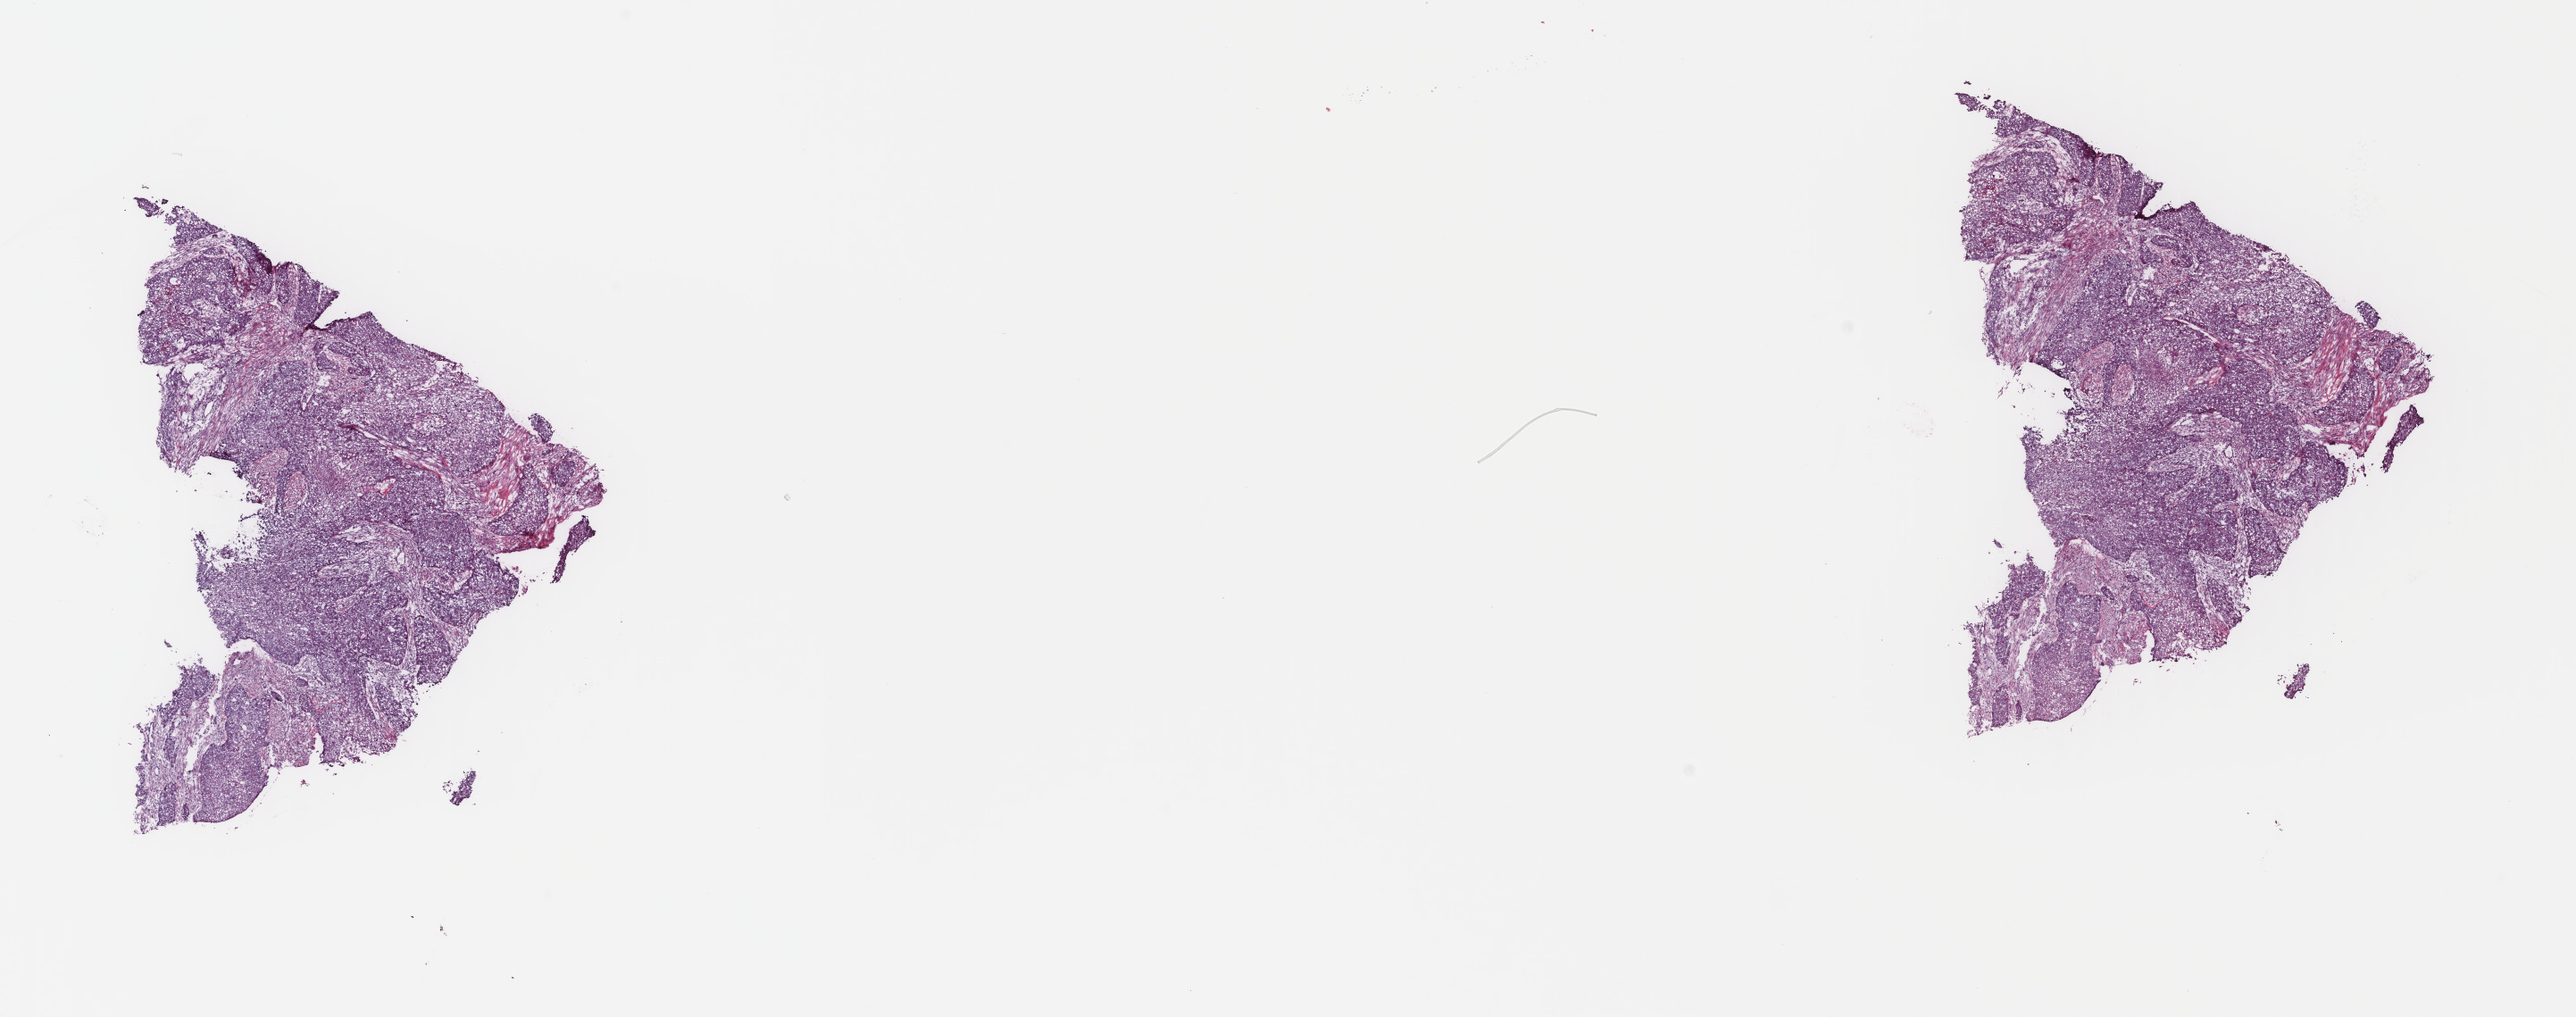
Whole-slide histology image, H&E-stained, a low-resolution overview of the entire scanned area, about 22.9 x 9.0 mm (slide scanned at 40x). Frozen section from the top of the tissue portion. Sample: primary tumour, bladder. Male, age 86 years at initial diagnosis. Histologic grade: high grade. Composition of this section per pathologist review: tumour cells 70%, tumour nuclei 85%, normal cells 0%, stromal cells 26%, necrosis 4%. Infiltration values recorded for this section: lymphocyte infiltration 2%, monocyte infiltration 0%, neutrophil infiltration 1%.
- AJCC pathologic stage: IV
- TNM: T2b N1 MX
- diagnosis: Transitional cell carcinoma (posterior wall of bladder)